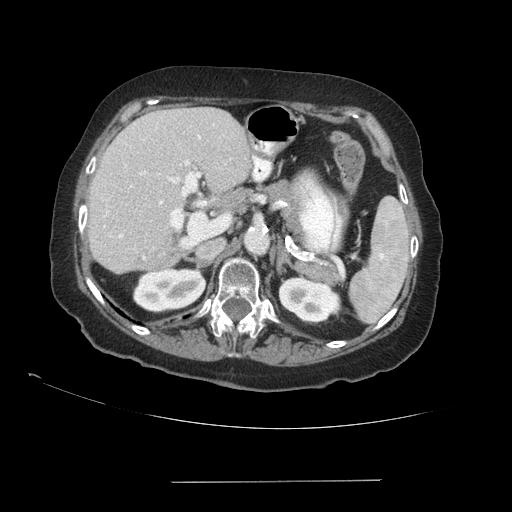
Contrast-enhanced abdominal CT (liver protocol), one axial slice; slice 56 of 89 in the series (ordered by position); reconstruction kernel STANDARD; soft-tissue window (W 400 / L 40 HU); 512 × 512 image matrix, field of view 400 × 400 mm. From the clinical record (not read from this slice): diagnosis: hepatocellular carcinoma (patient treated with transarterial chemoembolisation; whether this scan precedes or follows treatment is not stated here); TNM stage (as recorded): Stage-IVA; Child-Pugh class: A; tumour differentiation: poorly differentiated; tumour nodularity: uninodular.
Annotated regions visible in this slice (semi-automatically segmented with operator editing):
- liver parenchyma outside the tumour (the mass and vessels are separate outlines, so this box may not span the whole liver): bounding box (x1, y1, x2, y2) in pixels: (88, 108, 252, 272)
- liver vessels: (104, 135, 207, 259)